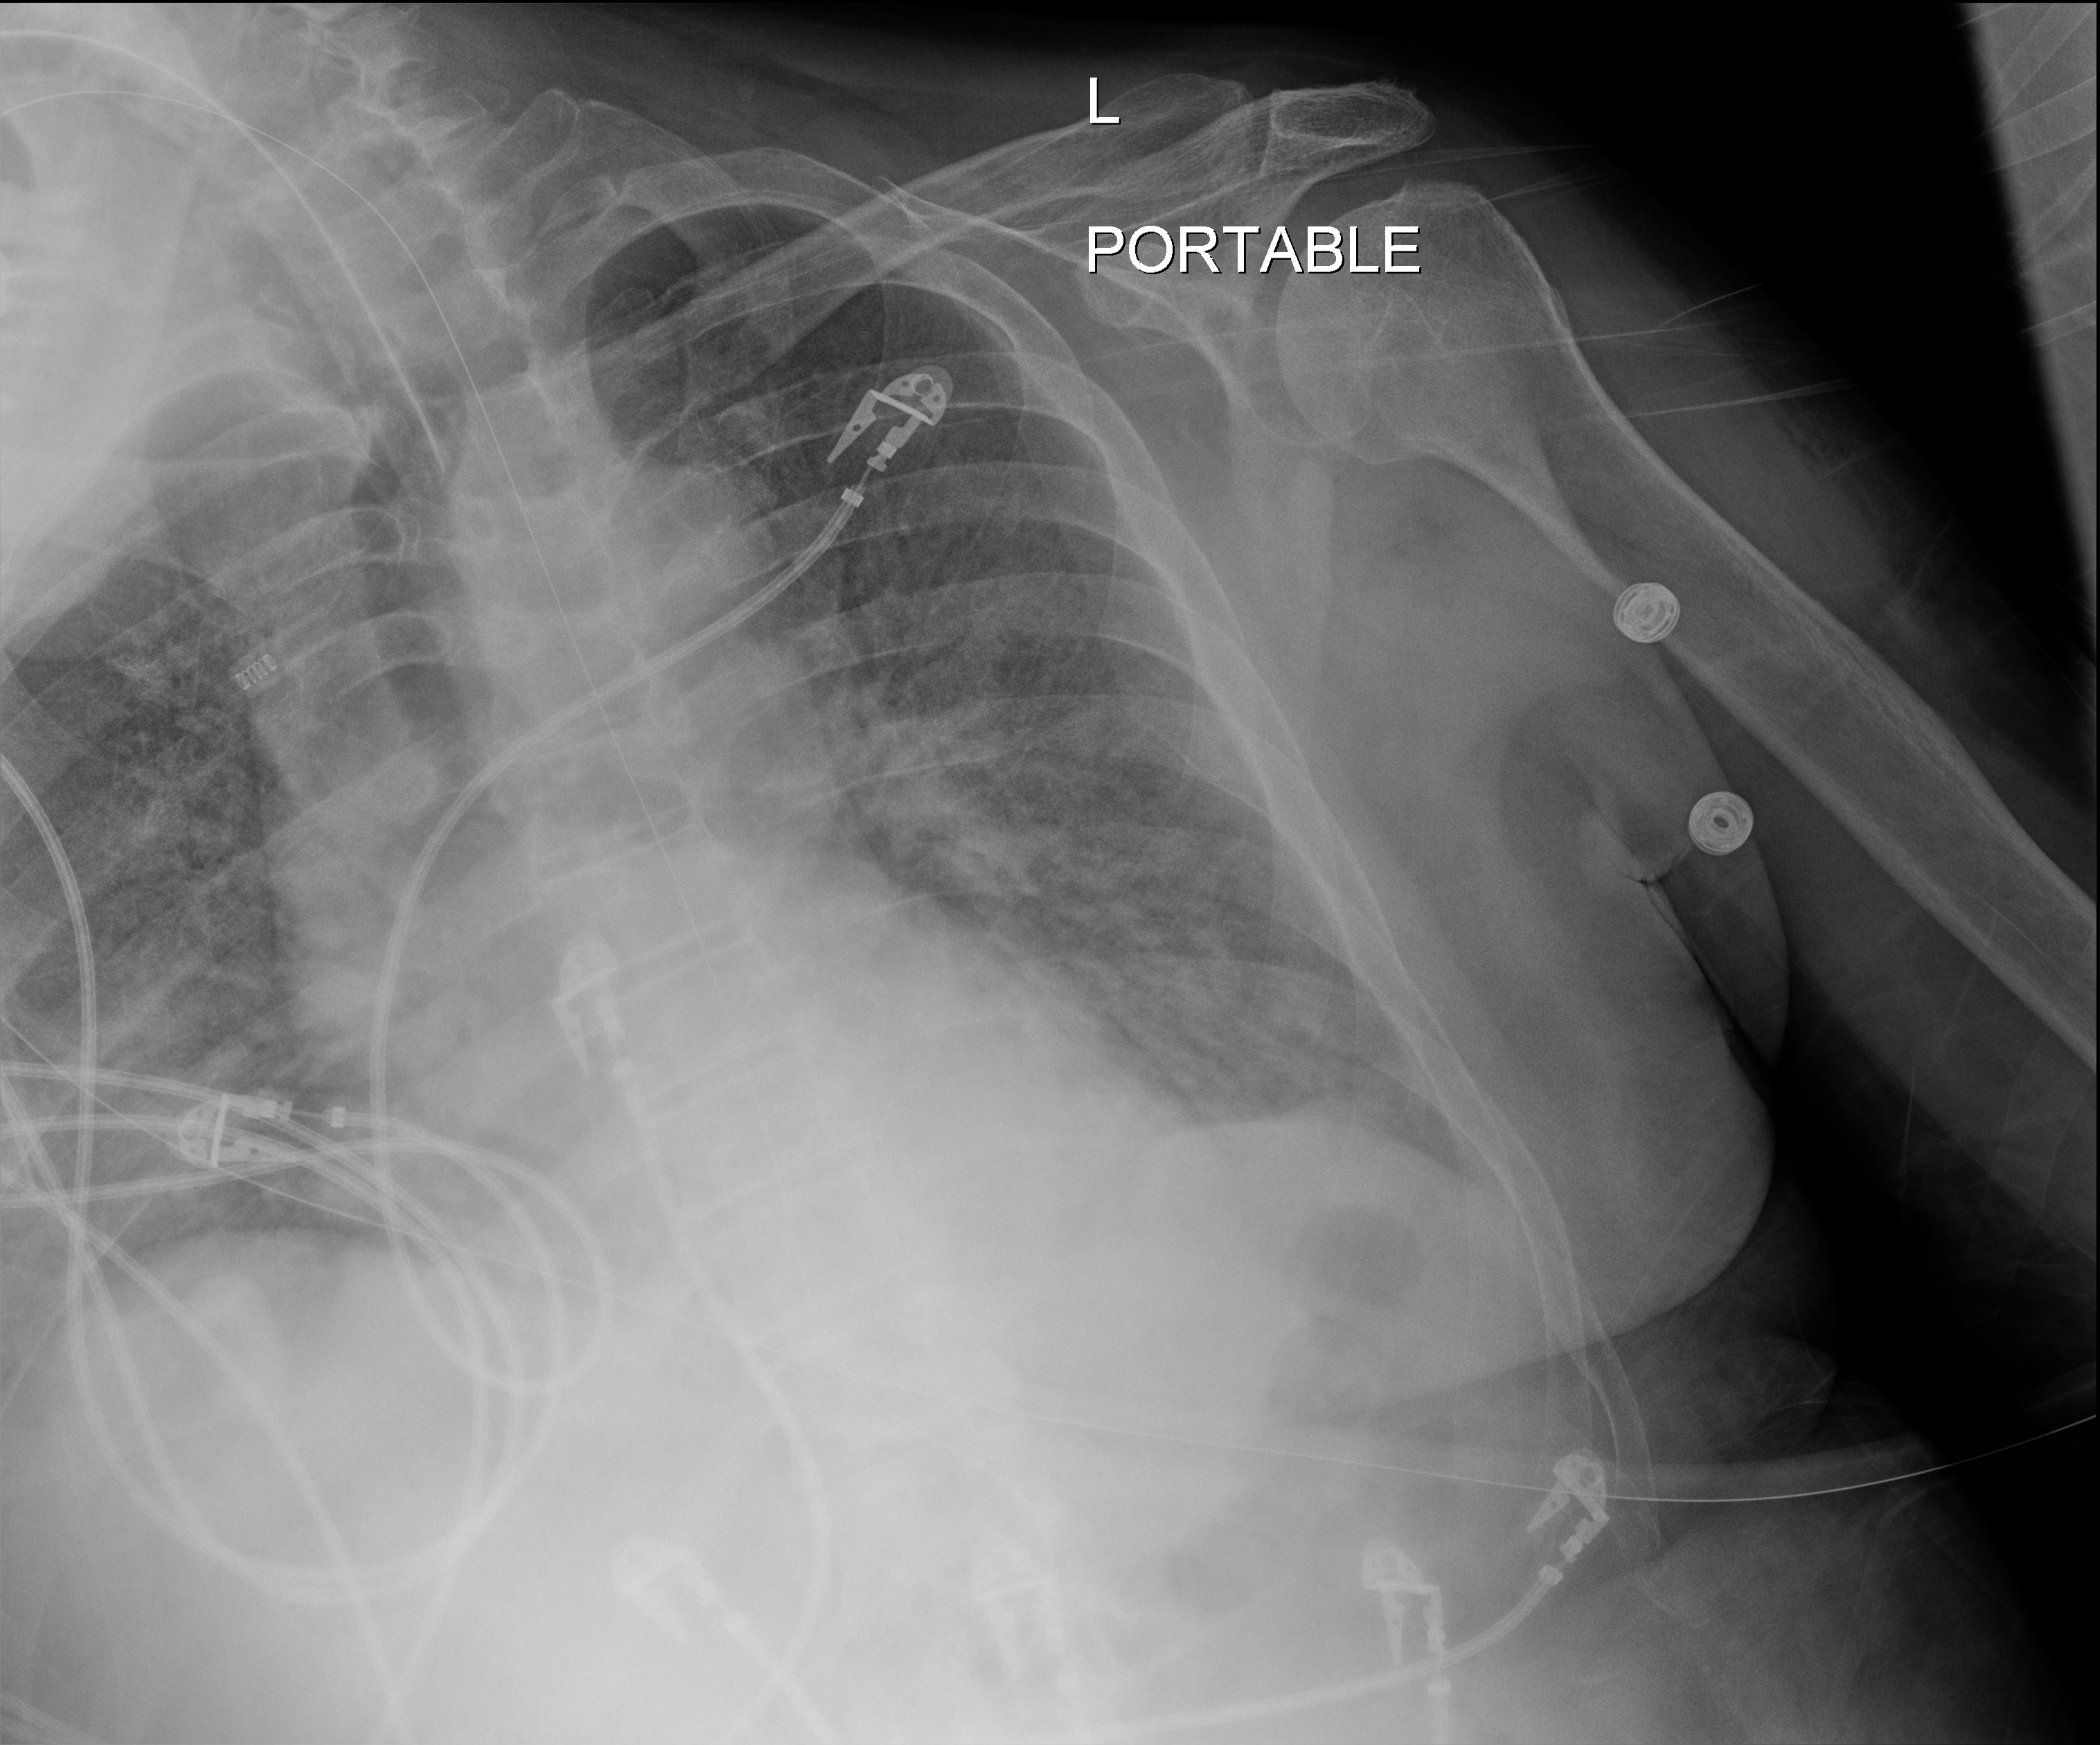
Portable chest radiograph; anteroposterior (AP) projection. Male patient hospitalised with COVID-19, age 60–74 years.
Admission-level facts for this patient (not findings on this image; timing relative to this image not recorded): length of hospital stay: 16 days.